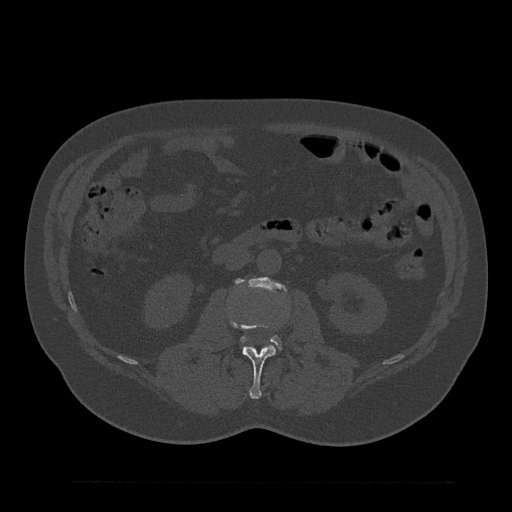
CT including the spine, one axial slice. Position 75 of 797 along the scan axis. Reconstruction kernel Br40s/3. Bone window (W 1800 / L 400 HU). 512 × 512 image matrix, field of view 430 × 430 mm. Patient: male, 61 years. Case-level facts recorded for this patient, not image findings: primary cancer: prostate.
Outlined on this slice (semi-automatic segmentation, software-assisted and operator-edited):
- L2 vertebra: box from (x=229, y=319) to (x=275, y=399) px
- L3 vertebra: (x=236, y=278)–(x=284, y=349)